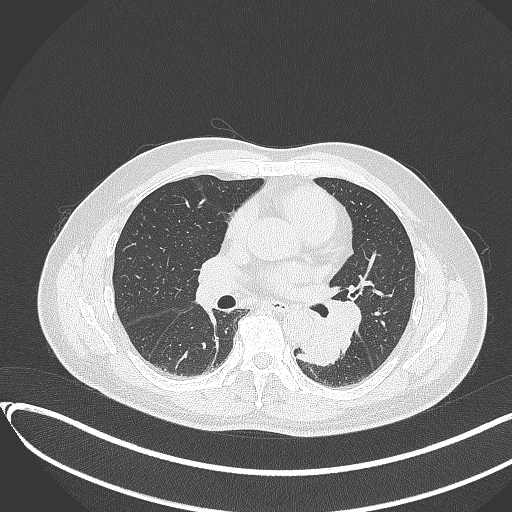
Chest CT, one axial slice; position 181 of 417 along the scan axis; reconstruction kernel B70f; 120 kVp; lung window (W 1500 / L -600 HU); 1 mm slice thickness; 512 × 512 image matrix, field of view 400 × 400 mm. Patient: male, 54 years. From the clinical record (not read from this slice): clinical TNM (as recorded): T3 N0 M0.
Structures marked on this image (rectangle marked by the reading radiologist):
- lung tumour (recorded histology: squamous cell carcinoma): box from (x=293, y=321) to (x=348, y=365) px